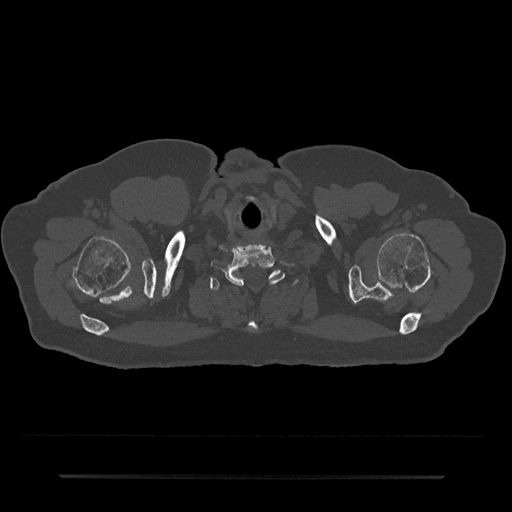
CT including the spine, one axial slice. Slice 662 of 797 in the series (ordered by position). Reconstruction kernel Br40s/3. 120 kVp. Bone window (W 1800 / L 400 HU). 512 × 512 image matrix. Male patient, age 69 years. From the clinical record (not read from this slice): primary cancer: prostate.
Structures marked on this image (semi-automatically segmented with operator editing):
- T1 vertebra: bounding box [x1, y1, x2, y2] px = [210, 270, 299, 330]